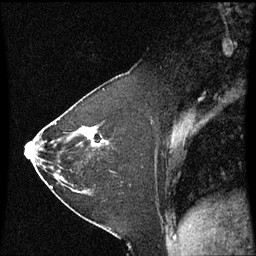
Breast MRI (dynamic contrast-enhanced), one sagittal slice. Dynamic contrast-enhanced series, image 2 of 3 at this slice position (ordered by acquisition). 1.5 T. TE 4.2 ms, TR 8.9 ms. 2 mm slice thickness. 256 × 256 image matrix, field of view 200 × 200 mm. Female patient, age 37 years. From the clinical record (not read from this slice): setting: breast cancer imaged before/during neoadjuvant chemotherapy; receptor status: HR-positive, HER2-negative.
Structures marked on this image (semi-automatically segmented with operator editing):
- analysis volume of interest (the breast-tissue region the enhancement analysis was run in; not a lesion): bounding box [x1, y1, x2, y2] px = [60, 102, 122, 181]
- tumour enhancement mask (voxels above the 70 % enhancement threshold inside the analysis volume of interest): [96, 128, 110, 145]